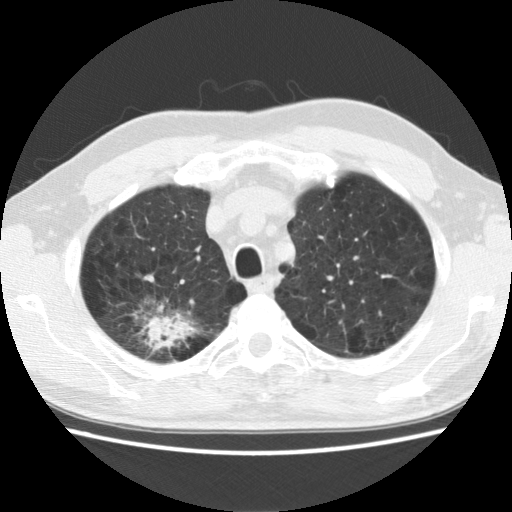
Chest CT (low-dose screening protocol), one axial image; baseline annual screen; lung window (W 1500 / L -600 HU); standard (soft-tissue) reconstruction kernel (STANDARD); 120 kVp; 512 × 512 image matrix. Male, age 64 years at enrolment.
• Lesion marked by an expert reader, bounding box <113,293,202,365> (left, top, right, bottom; pixels).
• The exam's reader record, not a measurement of the box and not confirmed to be the same lesion: non-calcified nodule or mass ≥4 mm, right upper lobe, 39 × 31 mm, spiculated (stellate) margins, mixed attenuation.
• Official screen result: positive, change unspecified: nodule(s) >= 4 mm or enlarging nodule(s), mass(es), or other non-specific abnormalities suspicious for lung cancer.
• Later outcome: lung cancer diagnosed 74 days after this screen — adenocarcinoma, NOS, right upper lobe, moderately differentiated (G2), stage IB (AJCC 6th edition), 40 mm at pathology.